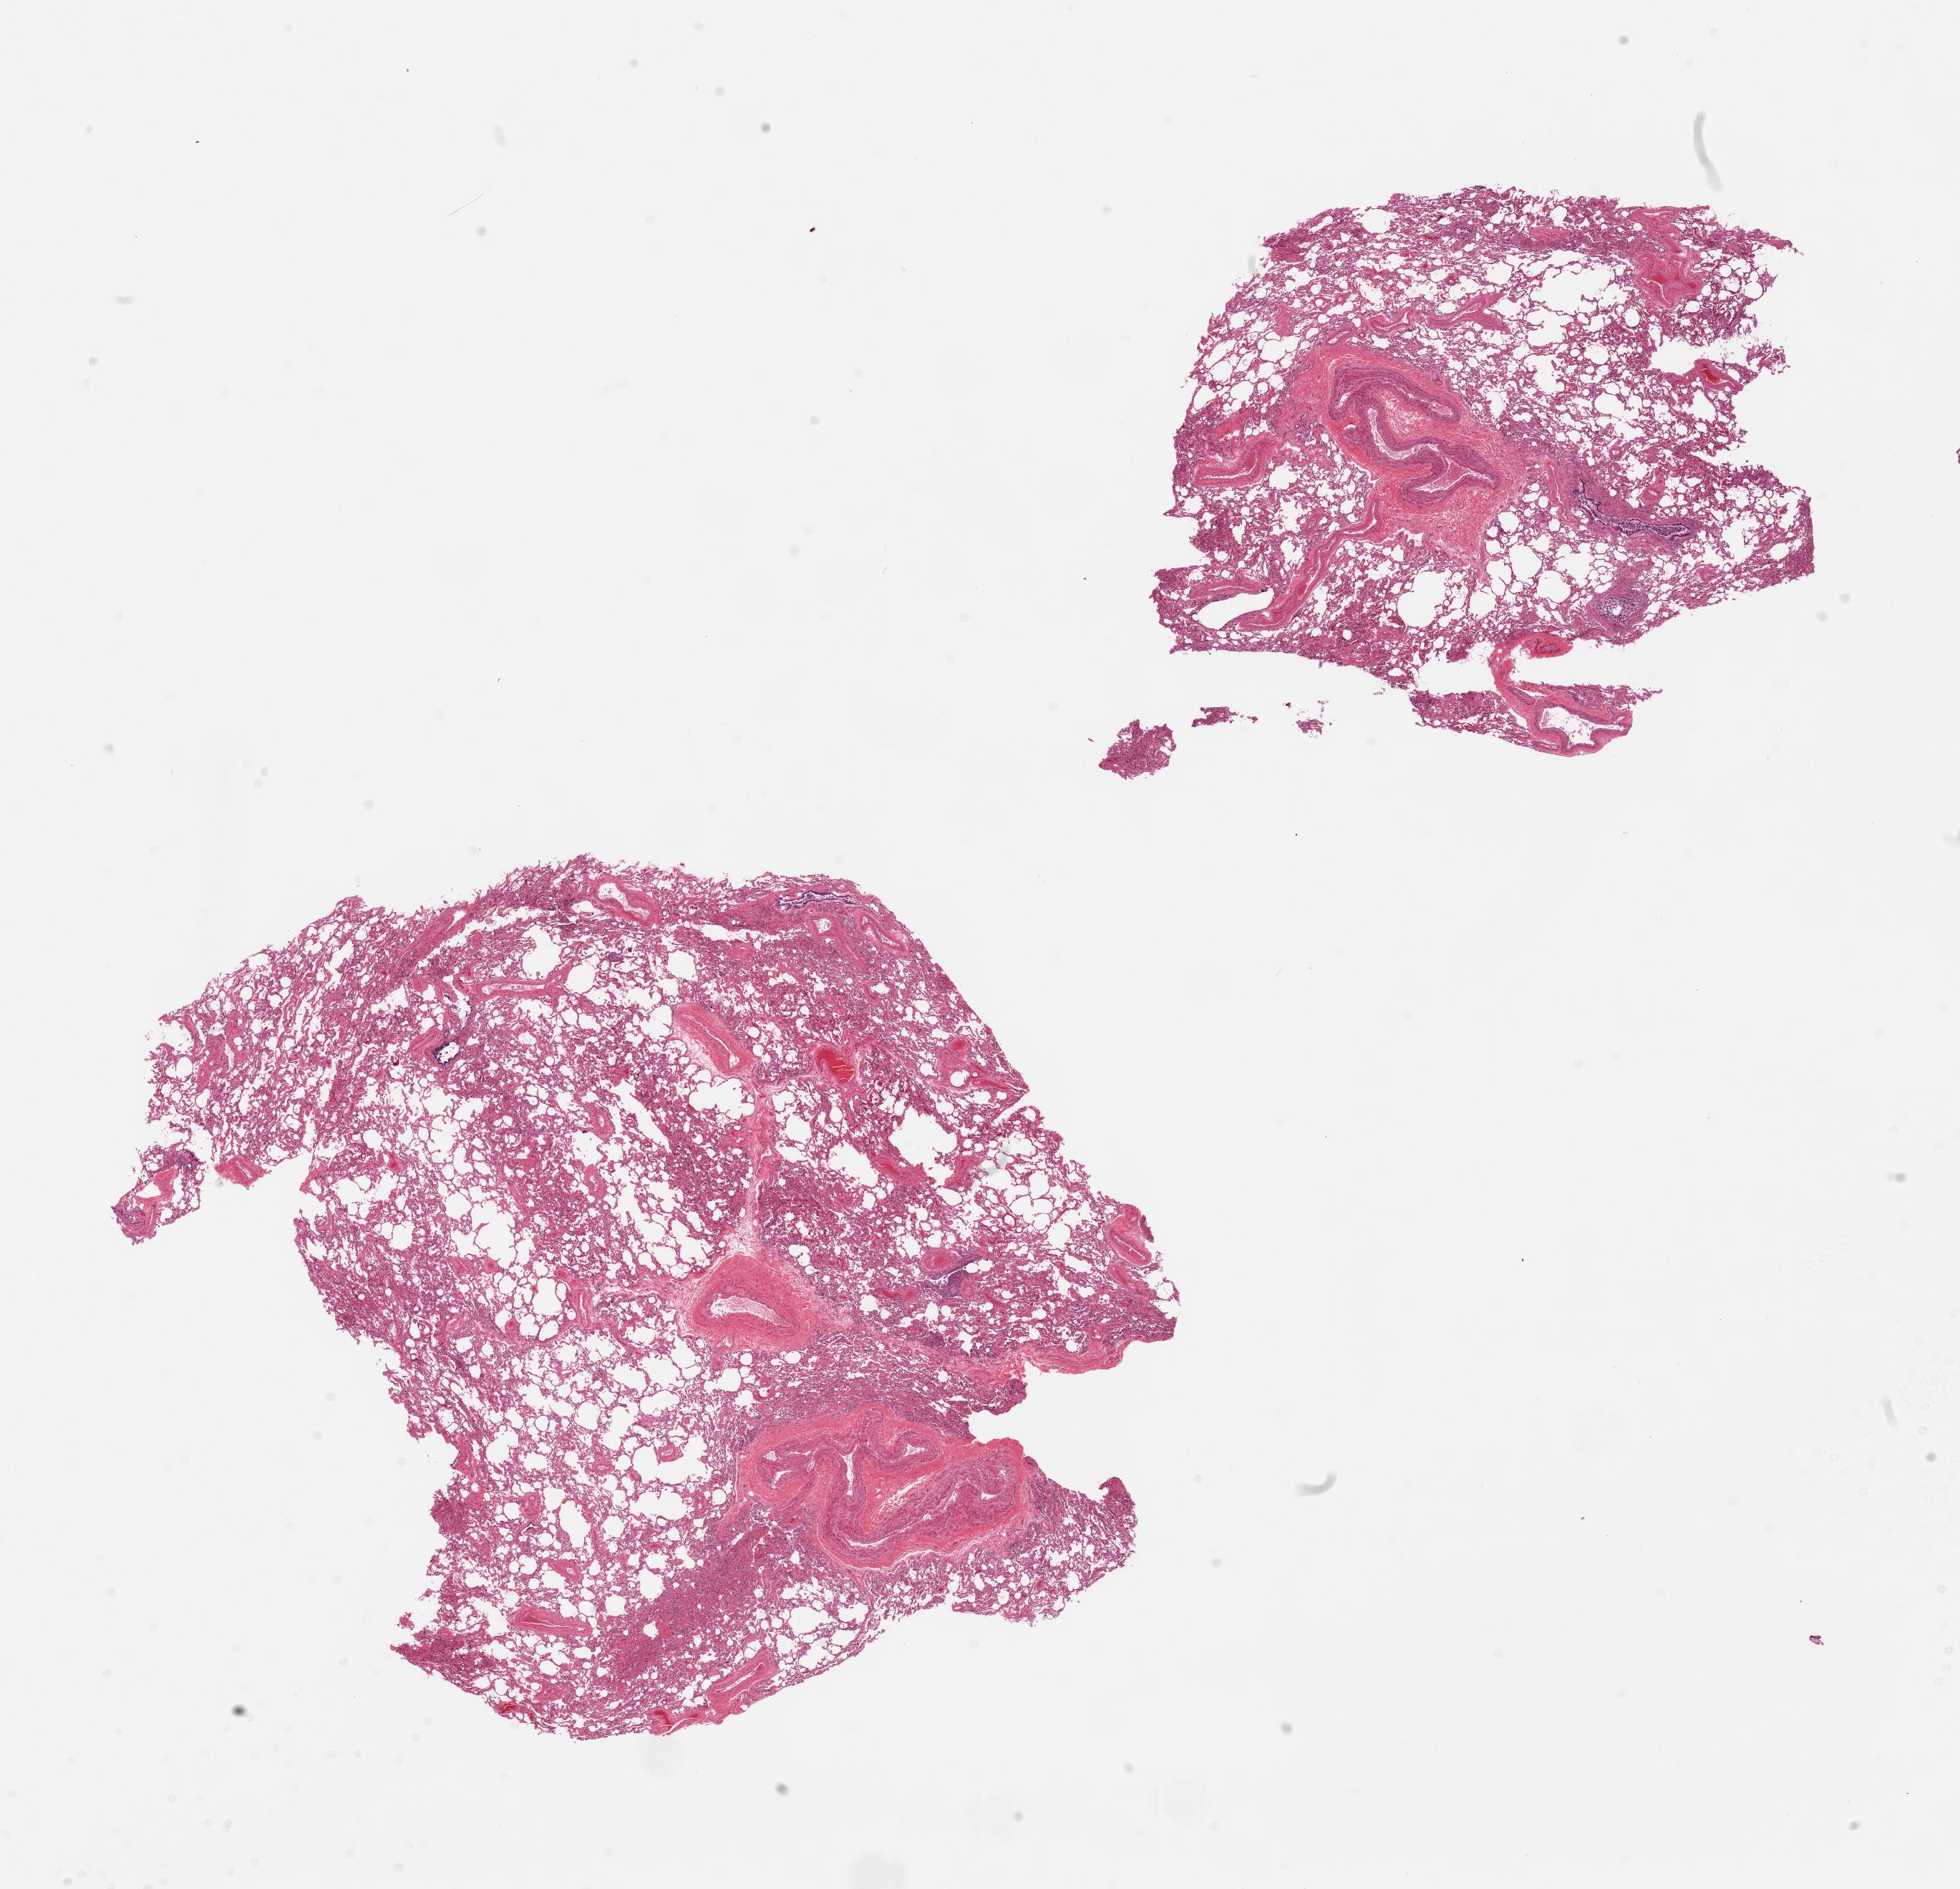
H&E whole-slide image, shown as a low-resolution overview of the whole scanned area (about 21.7 x 20.9 mm, acquisition: 20x scan); PAXgene-fixed paraffin-embedded (PFPE) section; target tissue: lung; tissue donor sample. Donor sex: male.
Review note (as recorded): 2 pieces, moderate congestion.